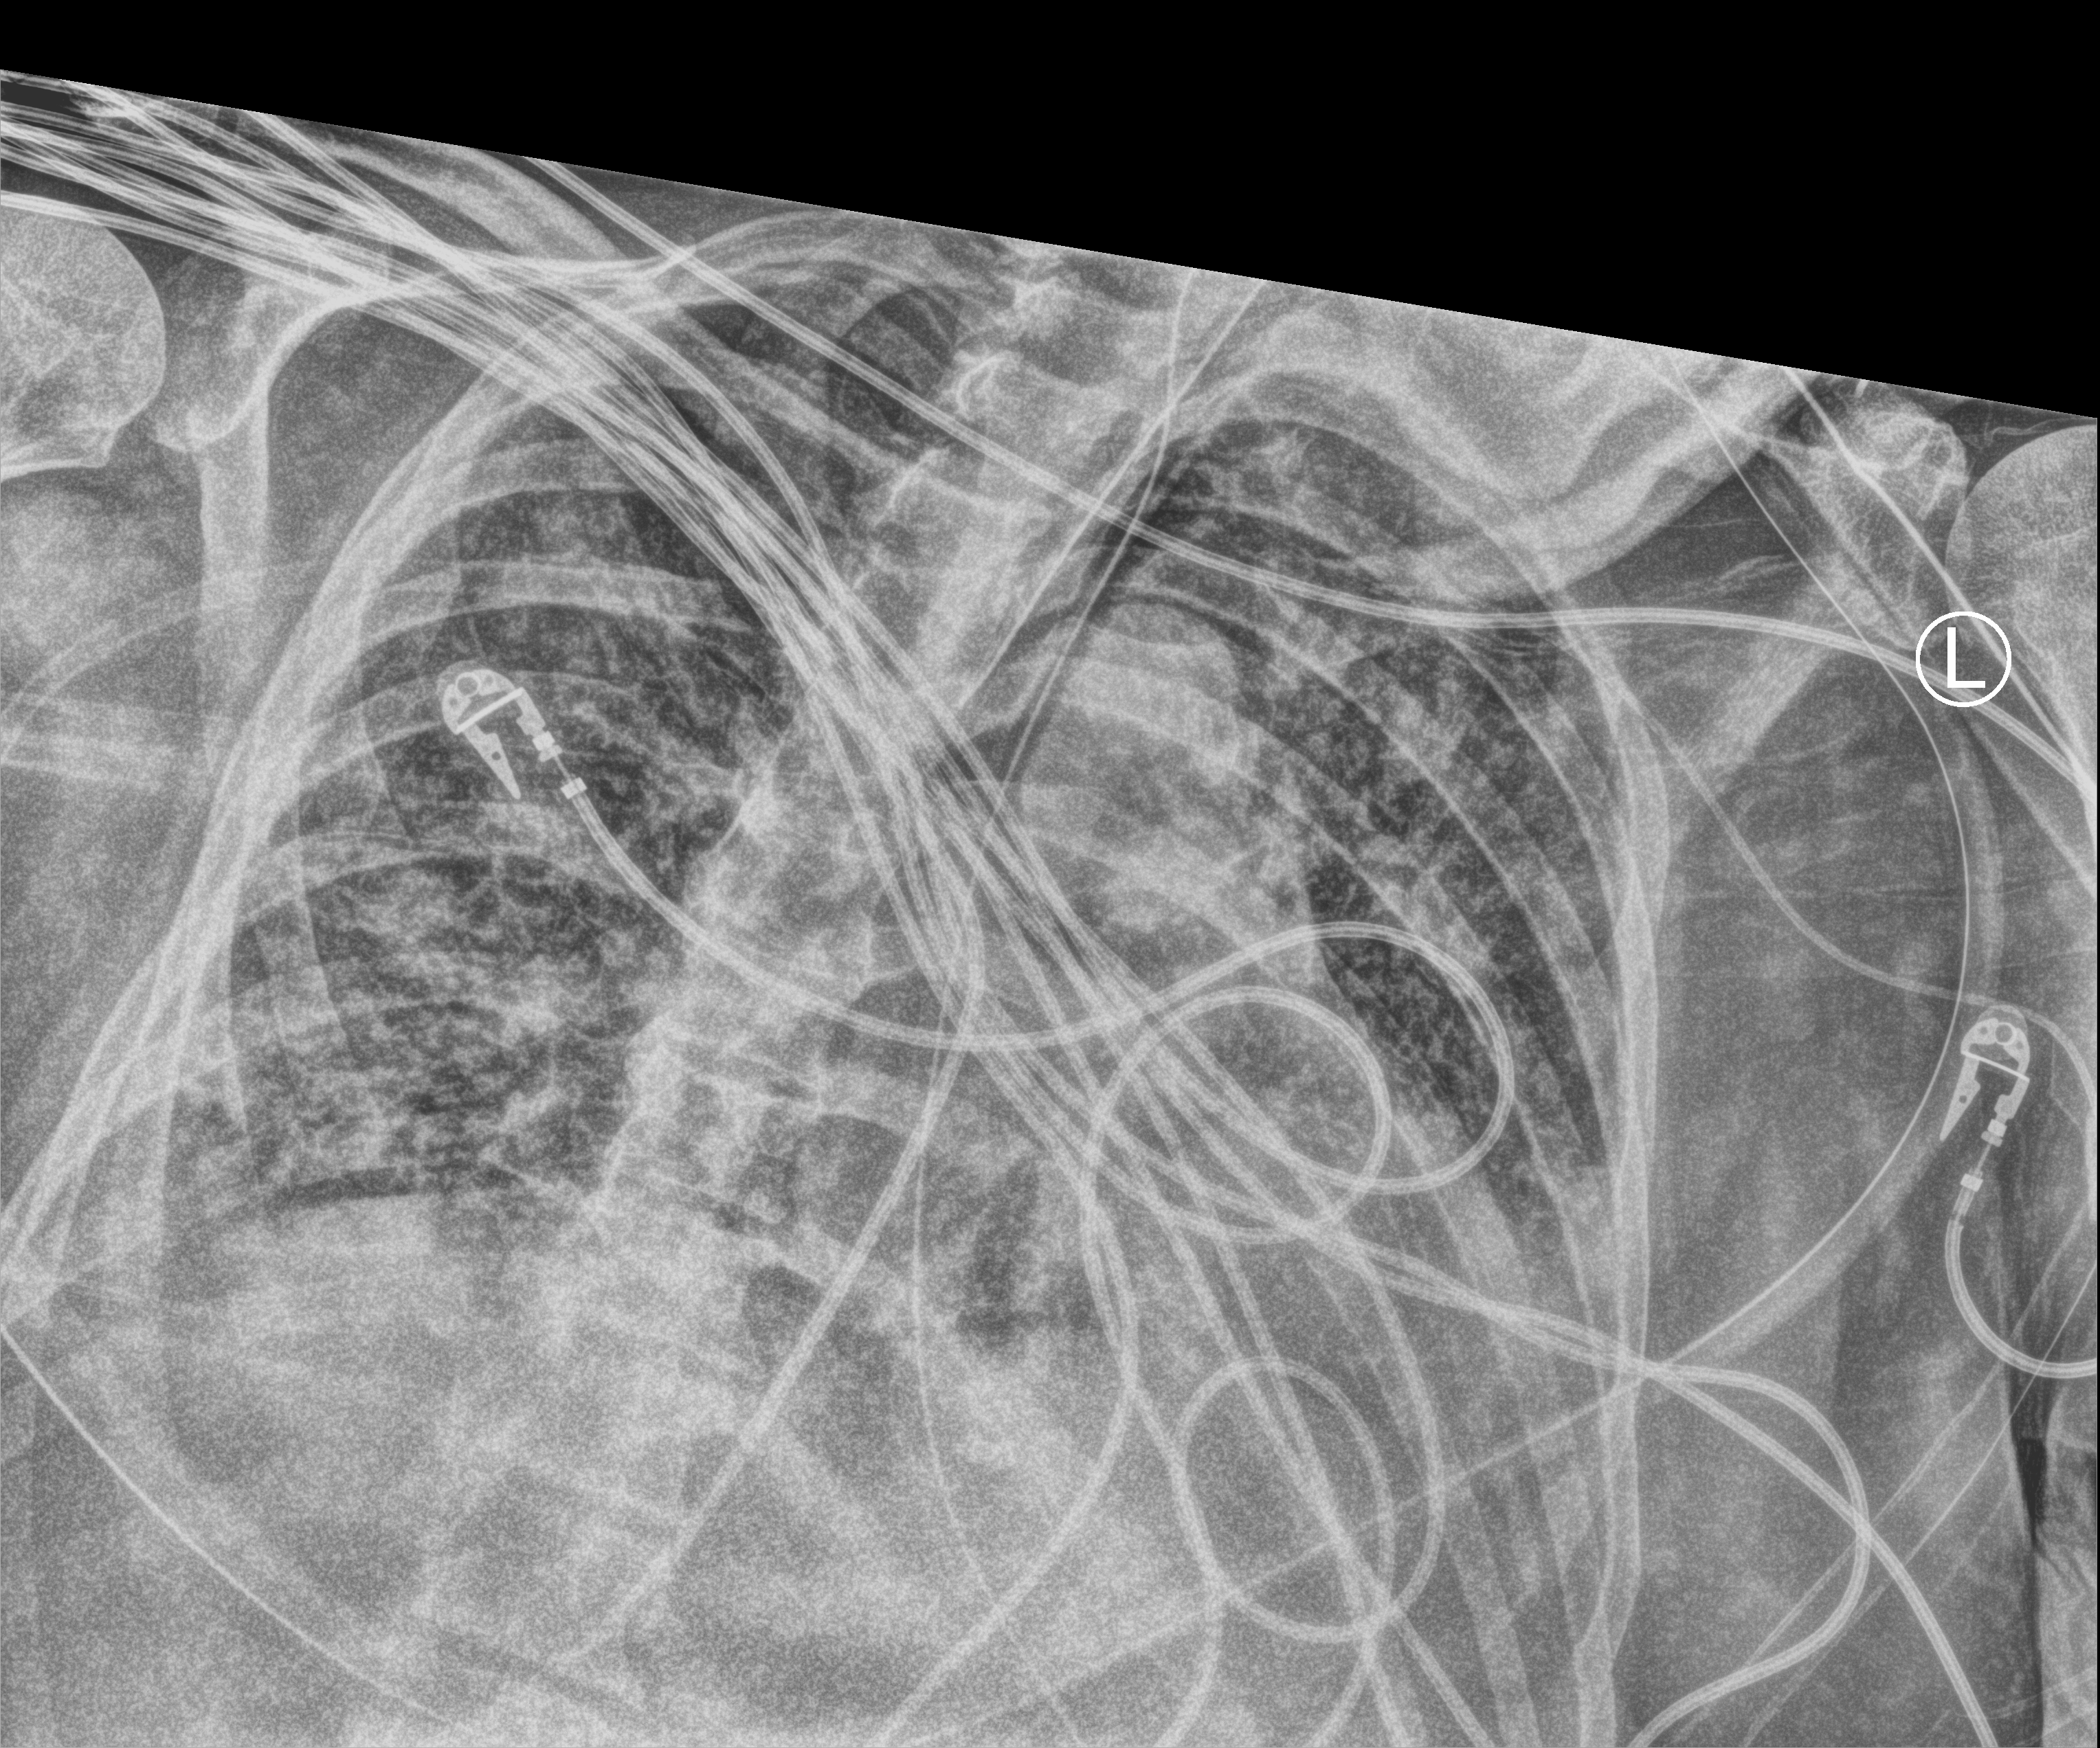
Bedside chest radiograph (computed radiography); anteroposterior (AP) projection. Male patient hospitalised with COVID-19, age 60–74 years.
From the hospital-stay record, not from the radiograph (when in the stay this image was taken is not recorded):
- mechanically ventilated during this hospital stay: yes